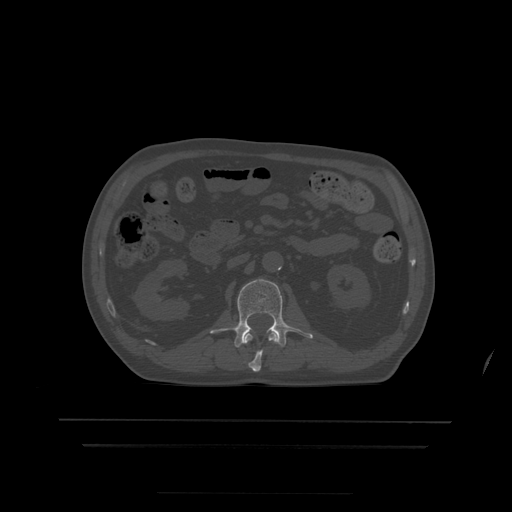
CT including the spine, one axial slice; position 152 of 522 along the scan axis; bone window (W 1800 / L 400 HU); 1.25 mm slice thickness; 512 × 512 image matrix. Patient age 68 years. From the clinical record (not read from this slice): primary cancer: urothelial.
Outlined on this slice (semi-automatic segmentation, software-assisted and operator-edited):
- L1 vertebra: bounding box <244,332,278,372> (left, top, right, bottom; pixels)
- L2 vertebra: <210,279,313,348>